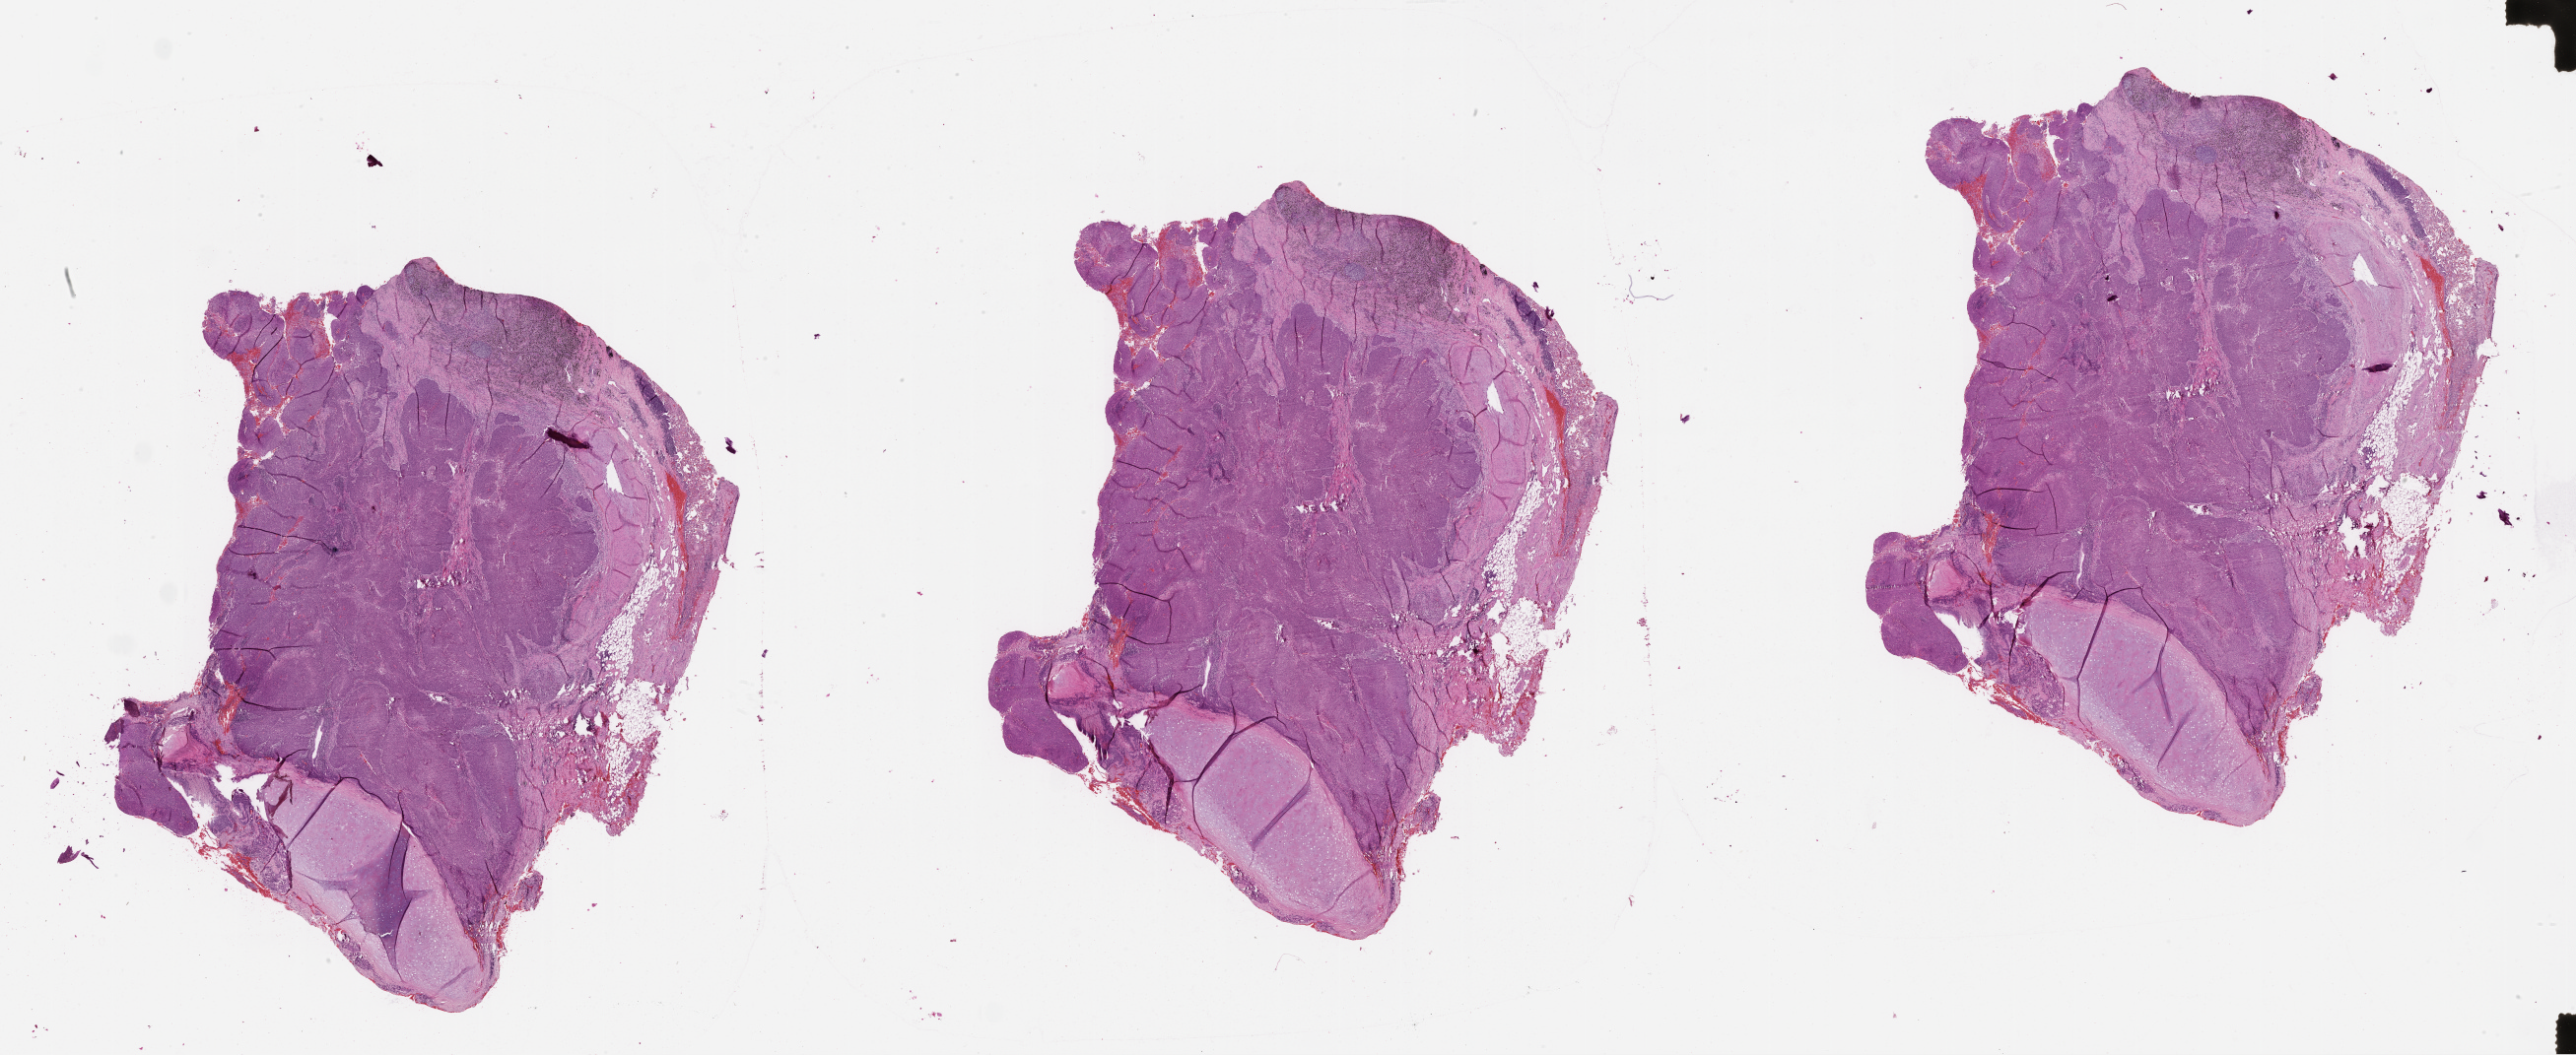
Hematoxylin and eosin (H&E) stained whole-slide image, low-resolution overview of the scanned area, about 42.1 x 17.2 mm. Lung, tumour tissue. Patient: male, age 71 years.
Patient diagnosis (cohort enrolment): squamous cell carcinoma (lung).